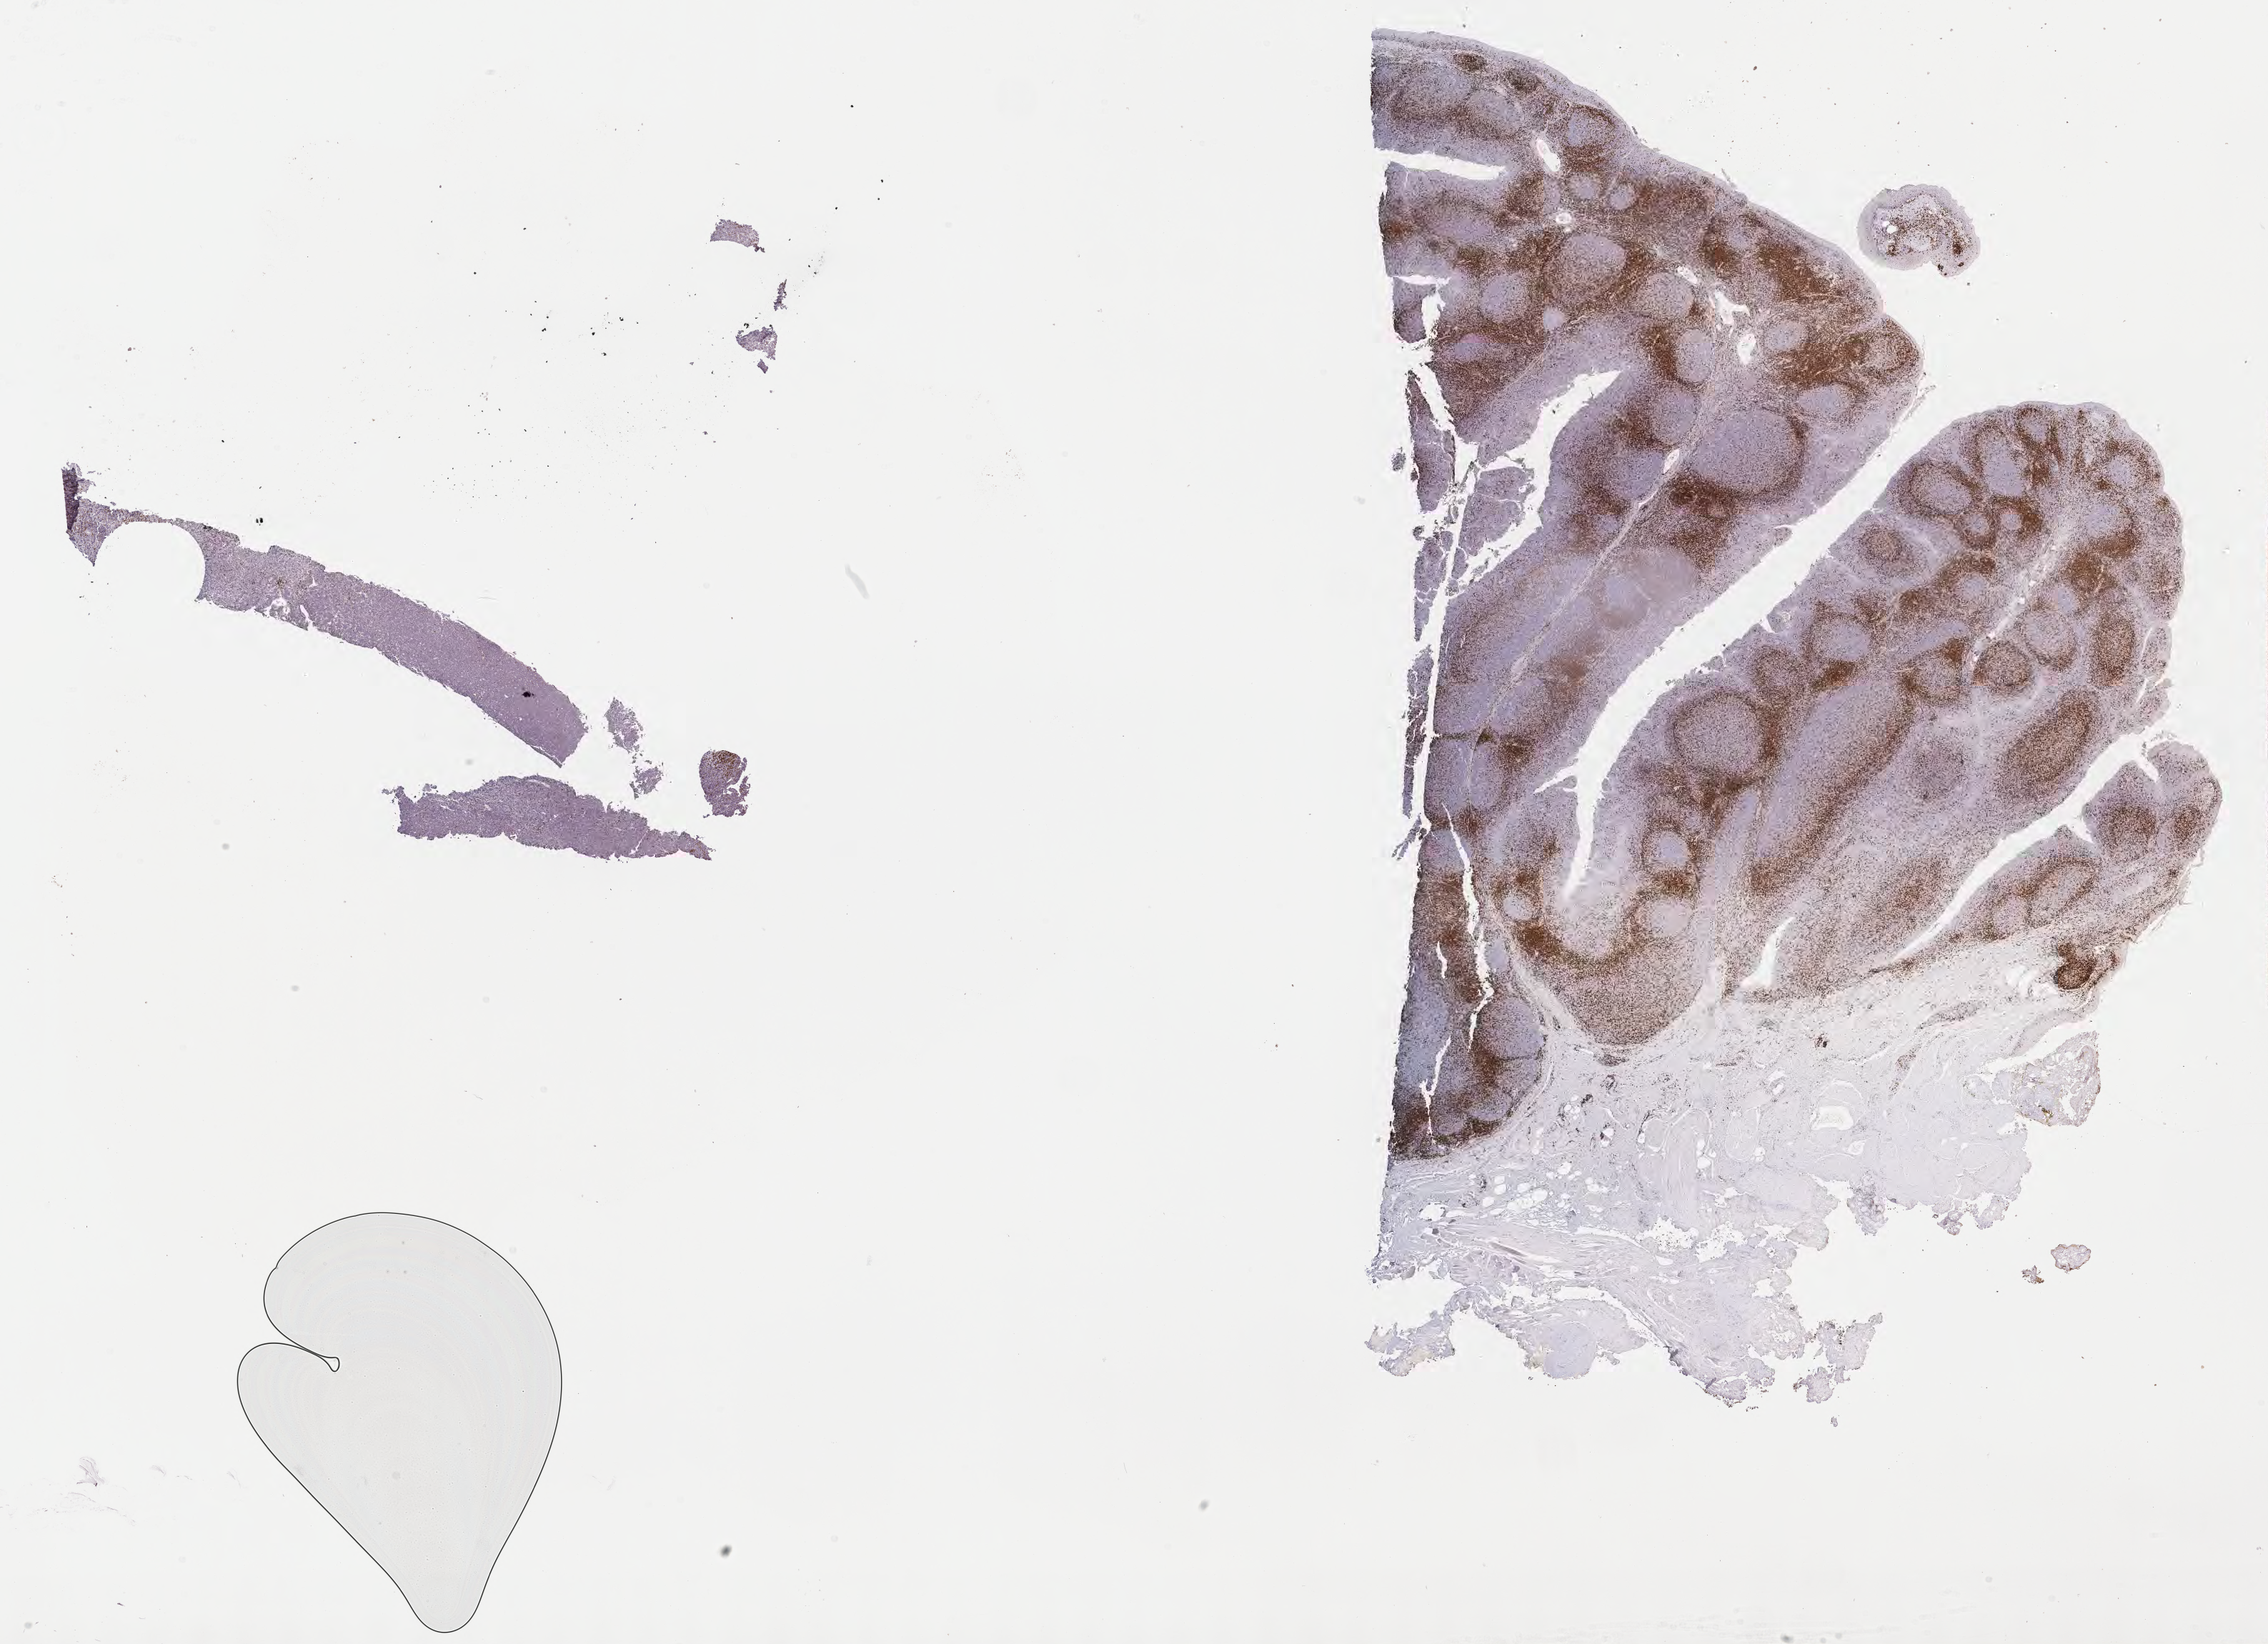
IHC for CD3, whole-slide image, shown as a low-resolution overview of the whole scanned area (about 25.7 x 18.6 mm). Tumor tissue. Site: liver. Male patient, age 15 years.
Diagnosis: Burkitt lymphoma, NOS.